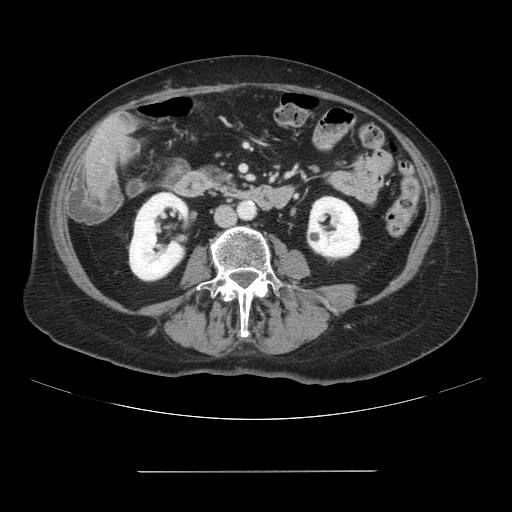
Contrast-enhanced abdominal CT, one axial slice; position 10 of 111 along the scan axis; 120 kVp; soft-tissue window (W 400 / L 40 HU); 2.5 mm slice thickness; 512 × 512 image matrix. Female patient, age 74 years. From the clinical record (not read from this slice): diagnosis: colorectal cancer liver metastases, imaged before liver resection; multiple liver metastases: yes; largest metastasis: 1.1 cm; disease in both lobes: yes.
Annotated regions visible in this slice (outlined manually by an expert reader):
- liver: box from (x=87, y=117) to (x=129, y=201) px